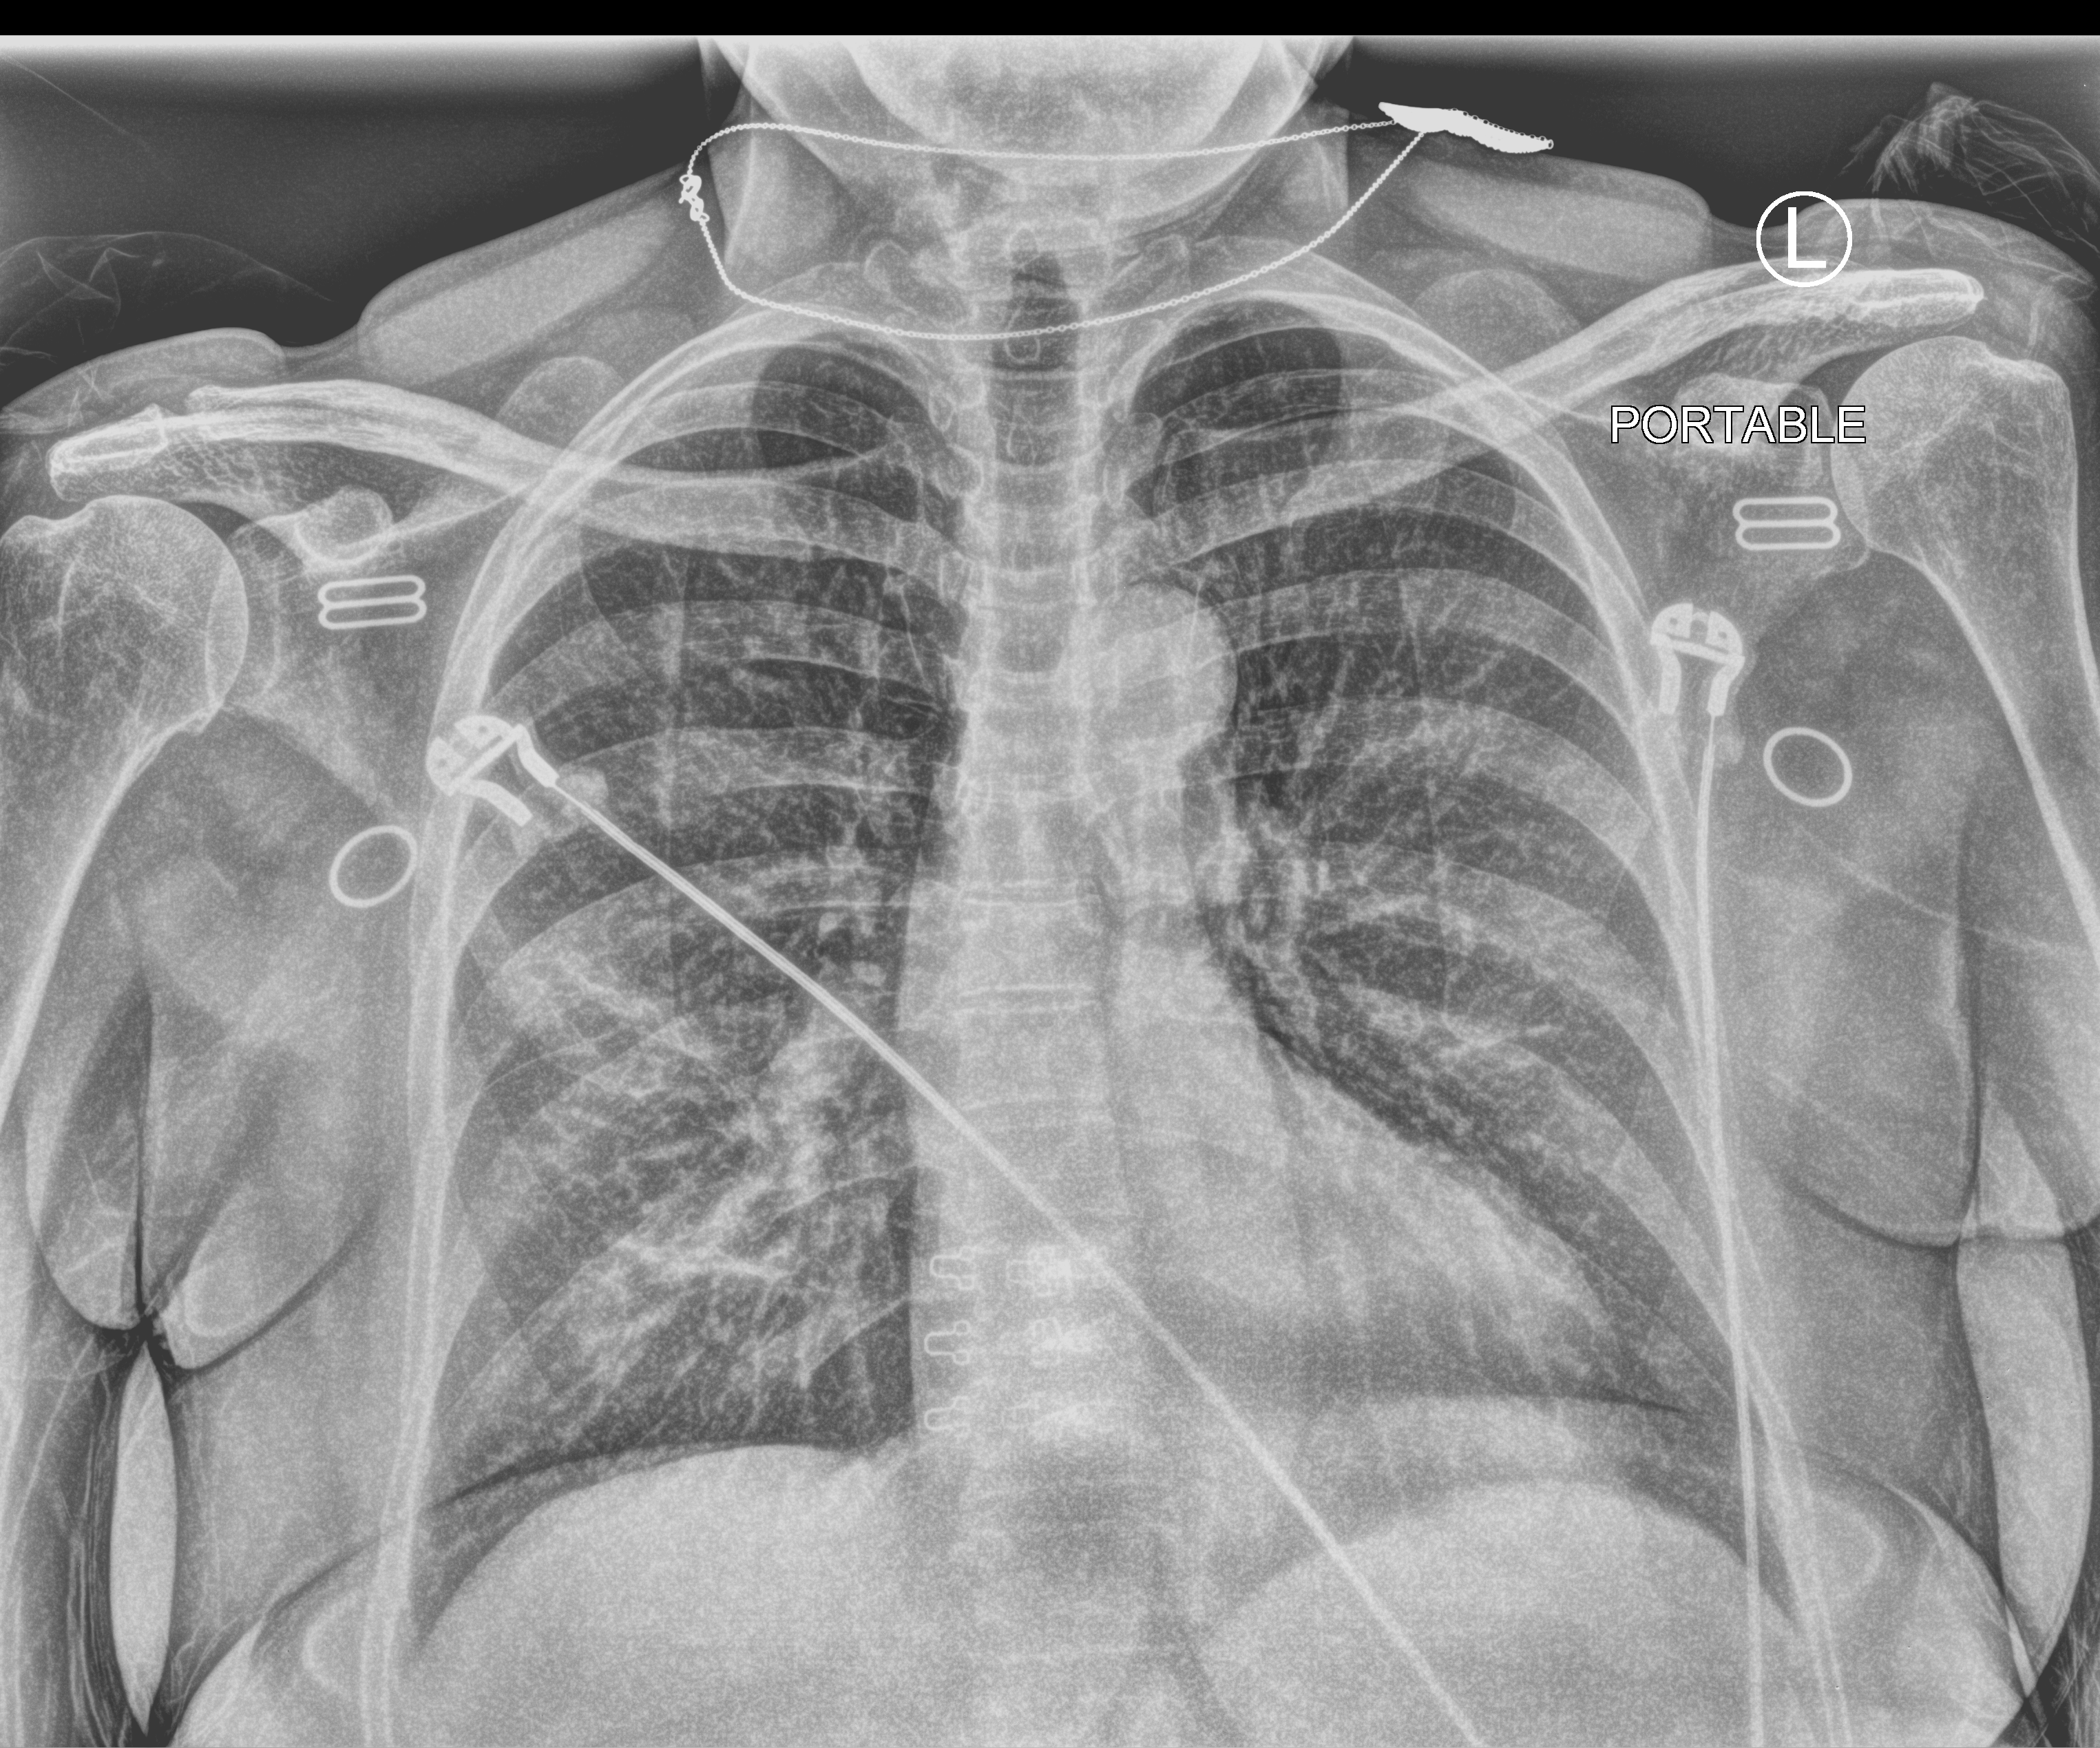
Bedside chest radiograph (computed radiography); anteroposterior (AP) projection. Female patient hospitalised with COVID-19, age 60–74 years.
Admission-level facts for this patient (not findings on this image; timing relative to this image not recorded):
- COPD (admission record): no
- hypertension (admission record): no